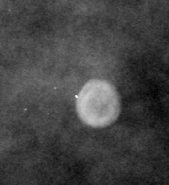
Cropped region of a digitized screen-film mammogram centred on a radiologist-marked abnormality; left breast; CC view; BI-RADS breast density category 3 (scale 1–4).
Calcifications, morphology round and regular / eggshell; BI-RADS assessment category 2; subtlety rating 3 on a 1 (subtle) to 5 (obvious) scale; benign; no additional work-up was recommended (benign without callback).